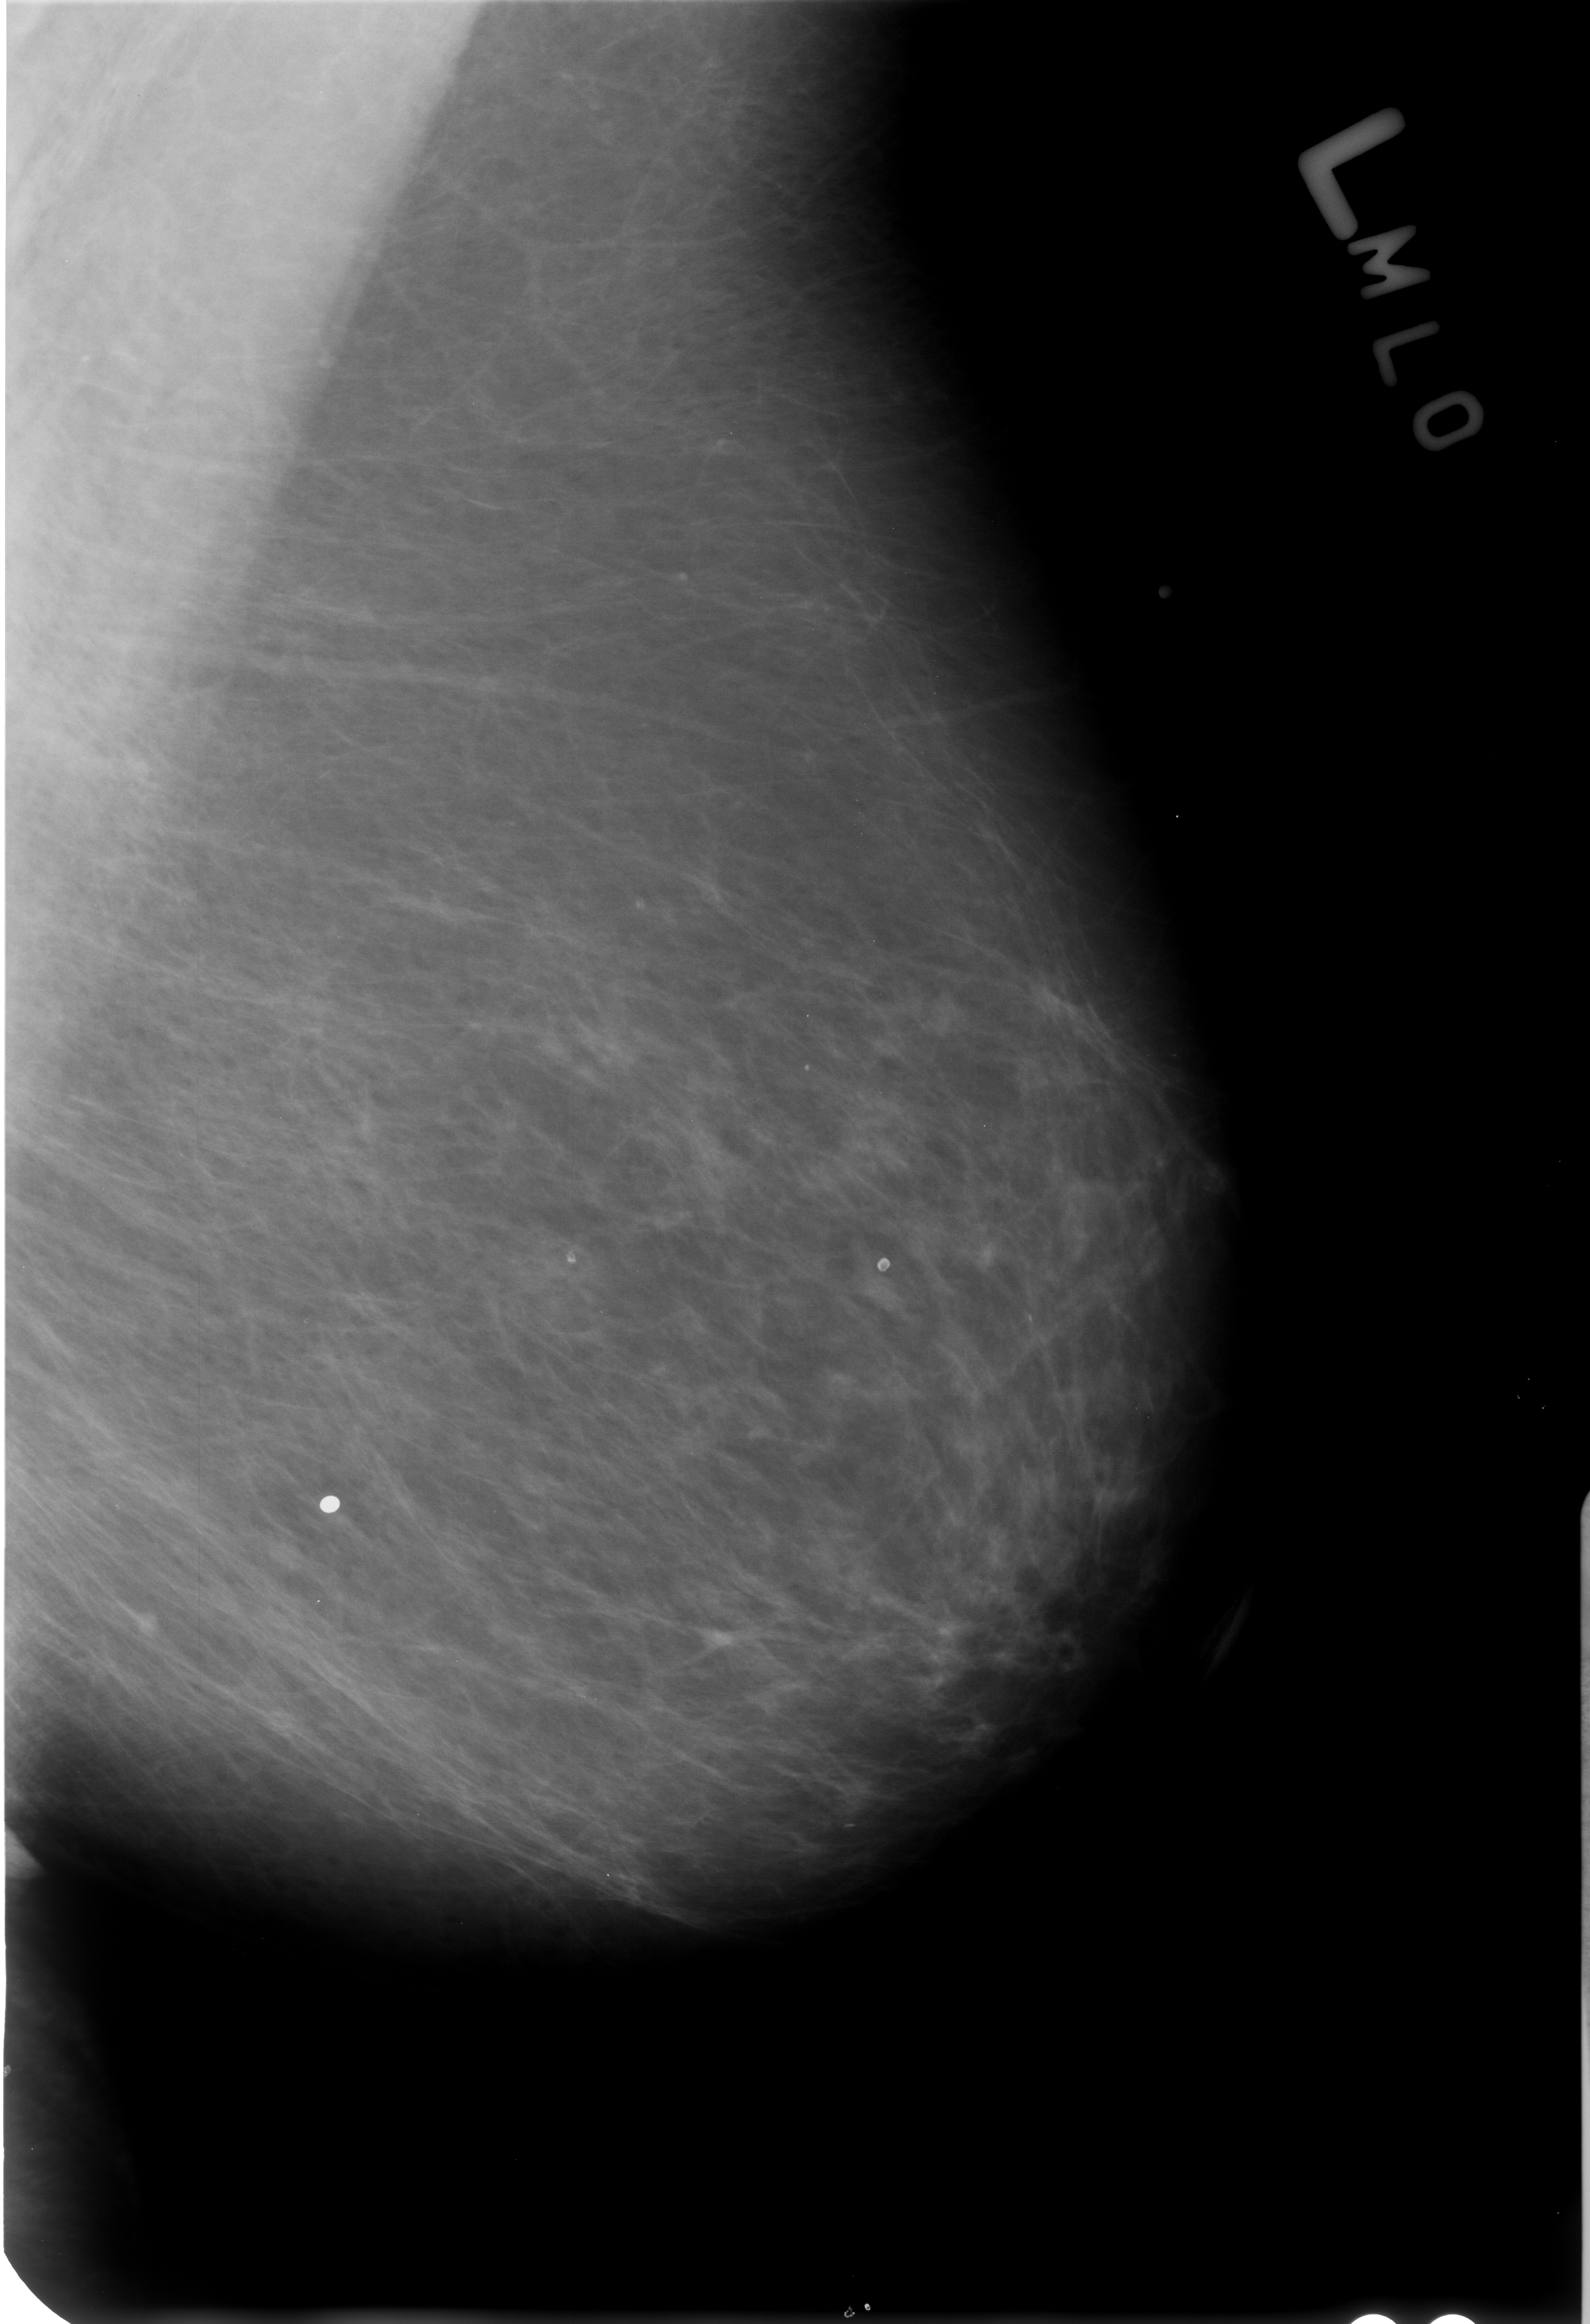
Digitized screen-film mammogram; left breast; mediolateral oblique (MLO) view; BI-RADS breast density category 1 (scale 1–4); 1590 × 2324 image matrix.
Expert-marked regions of interest on this image (one box per marked abnormality):
- Finding 1 of 2: calcifications, morphology lucent center; BI-RADS assessment category 2; benign; no additional work-up was recommended (outcome (as recorded, no biopsy): benign without callback): bounding box (x1, y1, x2, y2) in pixels: (558, 1235, 592, 1281)
- Finding 2 of 2: calcifications, morphology lucent center; BI-RADS assessment category 2; outcome (as recorded, no biopsy): benign without callback (not worked up further): (856, 1239, 914, 1298)